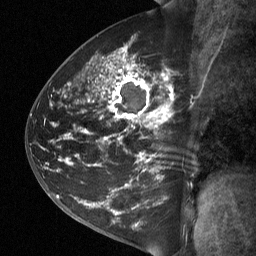
Breast MRI (dynamic contrast-enhanced), one sagittal slice. Slice 36 of 64 in the series (ordered by position). Dynamic contrast-enhanced study with each time point stored as its own series, time point 2 of 3 at this slice position (early post-contrast, ordered by acquisition time). 1.5 T. TE 4.8 ms, TR 27 ms. 2 mm slice thickness. 256 × 256 image matrix, field of view 200 × 200 mm. Patient: female, 42 years. Case-level facts recorded for this patient, not image findings: setting: breast cancer imaged before/during neoadjuvant chemotherapy; receptor status: triple-negative.
Outlined on this slice (semi-automatic segmentation, software-assisted and operator-edited):
- analysis volume of interest (the breast-tissue region the enhancement analysis was run in; not a lesion): bounding box [x1, y1, x2, y2] px = [49, 45, 200, 197]
- tumour enhancement mask (voxels above the 90 % enhancement threshold inside the analysis volume of interest): [70, 53, 174, 186]